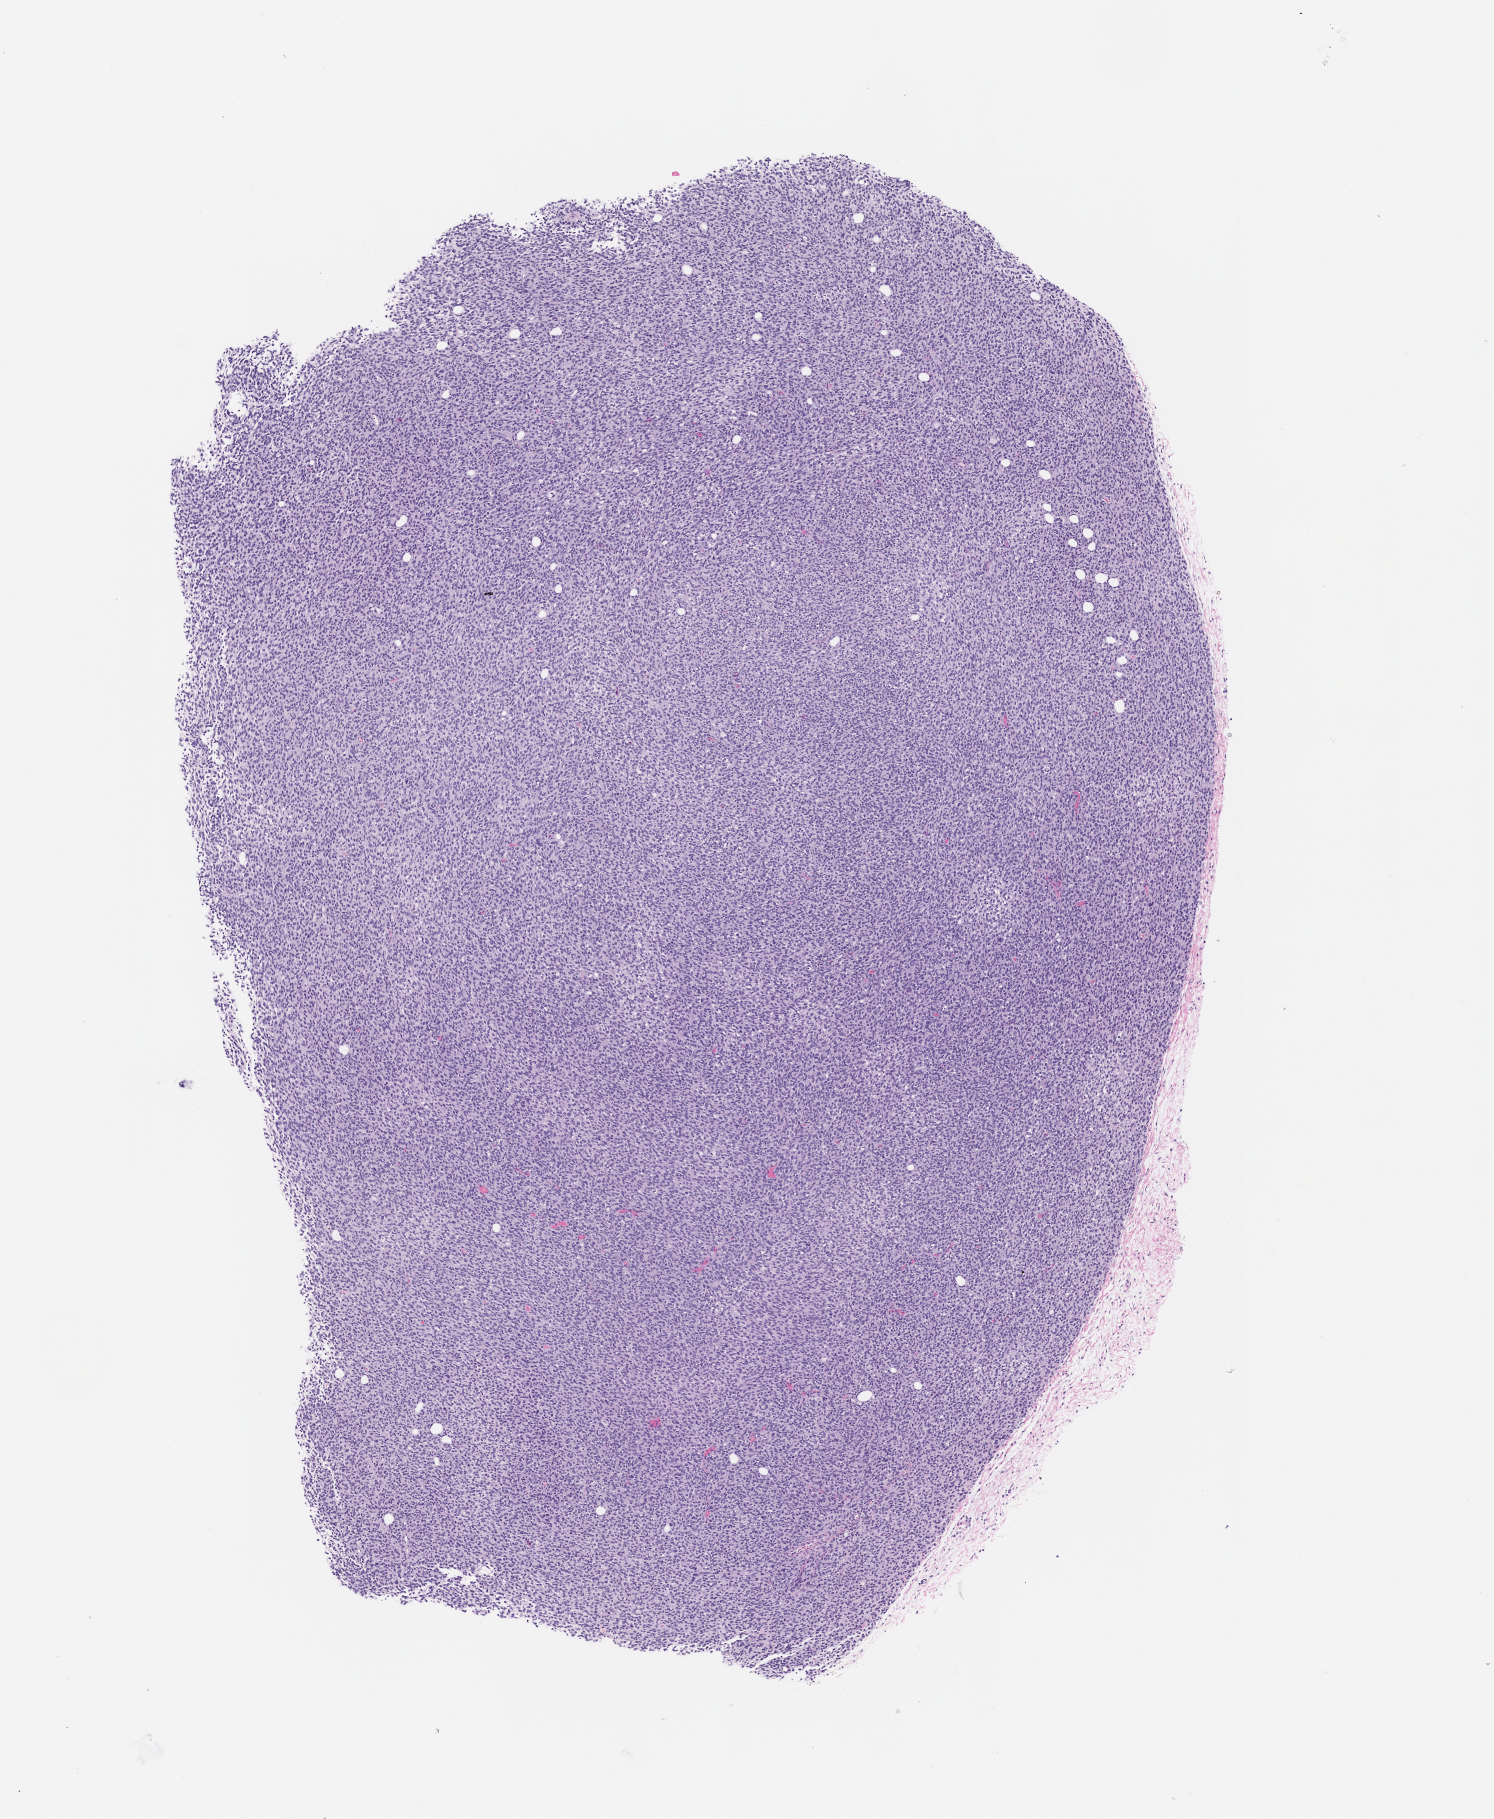
Hematoxylin and eosin (H&E) whole-slide image of a patient-derived xenograft (PDX) tumor grown in a mouse, low-resolution overview of the scanned area, about 6.0 x 7.3 mm; formalin-fixed, paraffin-embedded (FFPE) tissue; originating tumor site category: skin.
- originating patient diagnosis: Melanoma